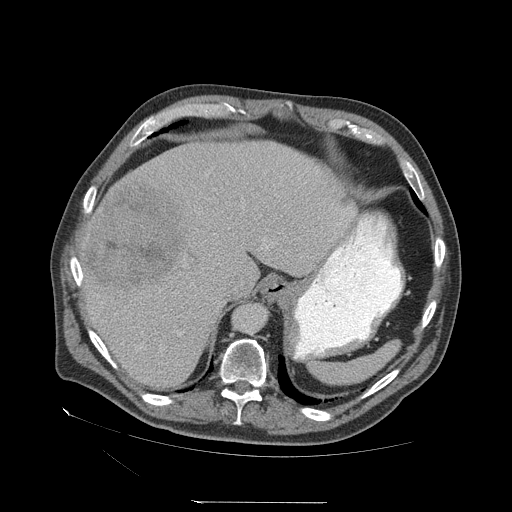
Contrast-enhanced abdominal CT (liver protocol), one axial slice. Slice 50 of 83 in the series (ordered by position). Reconstruction kernel STANDARD. Soft-tissue window (W 400 / L 40 HU). 2.5 mm slice thickness. 512 × 512 image matrix, field of view 460 × 460 mm. From the clinical record (not read from this slice): diagnosis: hepatocellular carcinoma (patient treated with transarterial chemoembolisation; whether this scan precedes or follows treatment is not stated here); TNM stage (as recorded): Stage-I; Child-Pugh class: A; tumour nodularity: uninodular.
Annotated regions visible in this slice (semi-automatic segmentation, software-assisted and operator-edited):
- liver parenchyma outside the tumour (the mass and vessels are separate outlines, so this box may not span the whole liver): bounding box <80,140,356,388> (left, top, right, bottom; pixels)
- mass: <85,182,185,297>
- liver vessels: <267,223,341,247>